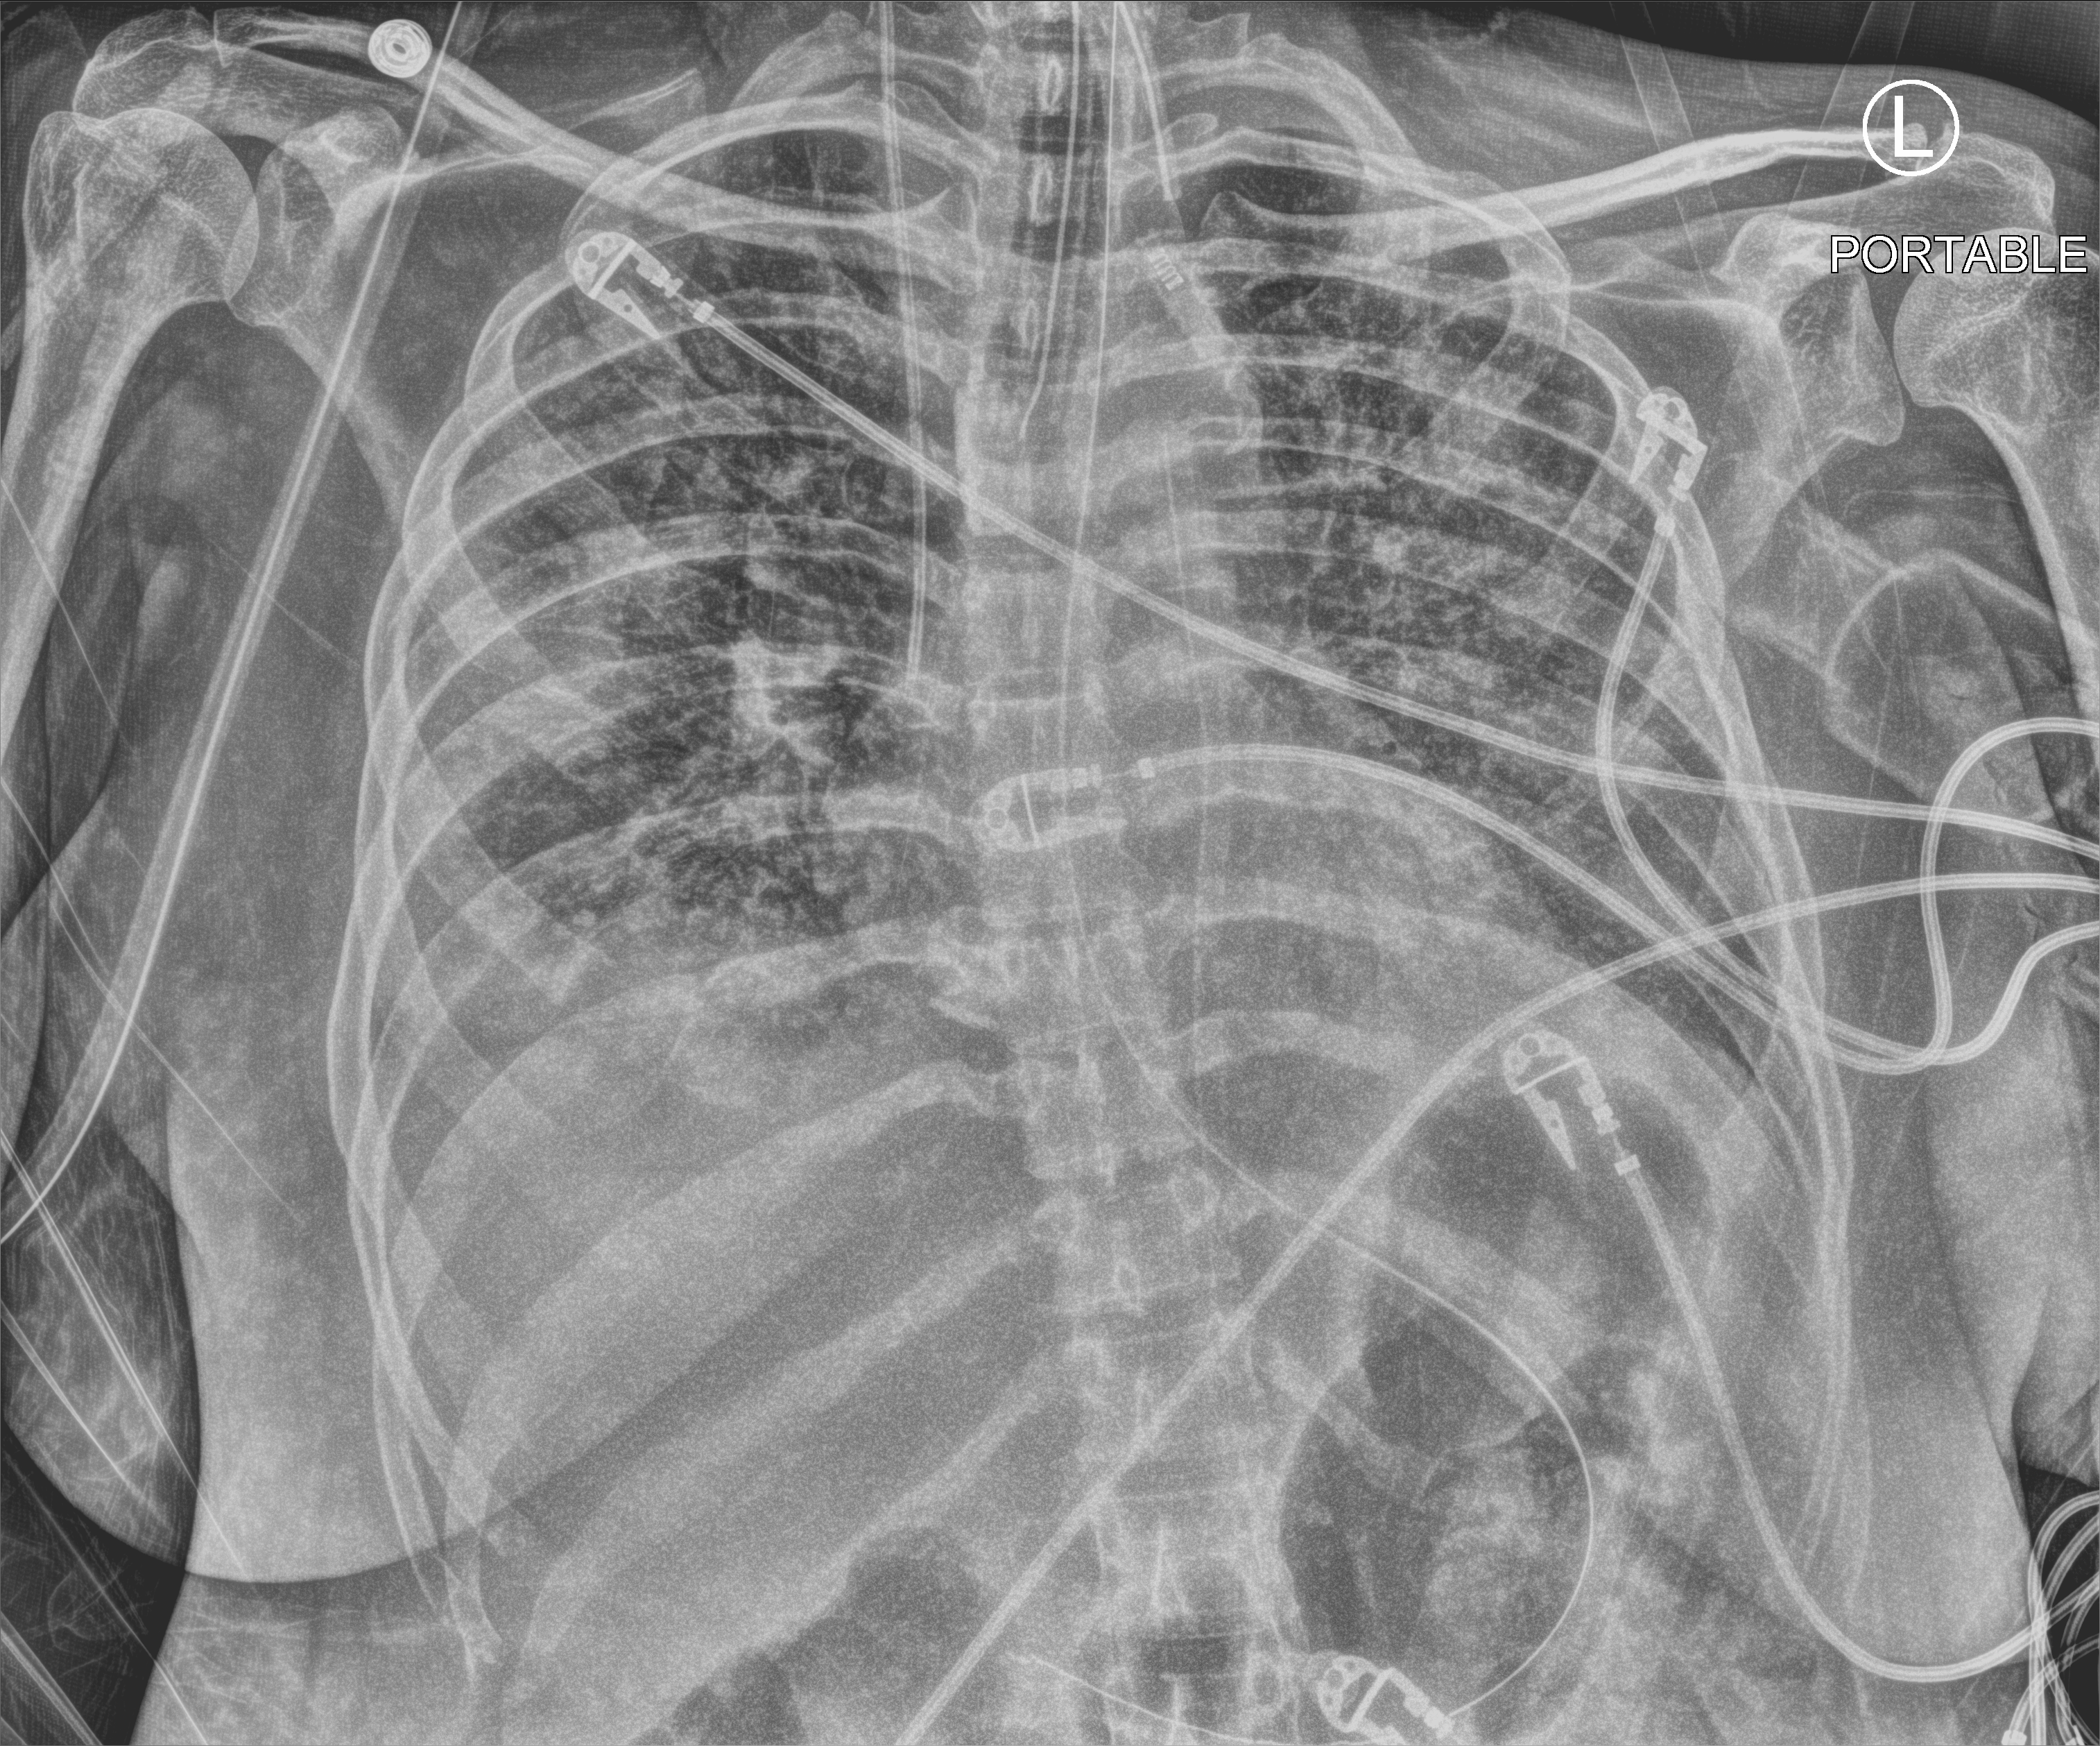
Chest X-ray (portable); anteroposterior (AP) projection. Adult patient hospitalised with COVID-19, age 18–59 years.
From the hospital-stay record, not from the radiograph (when in the stay this image was taken is not recorded): hypertension (admission record): no.